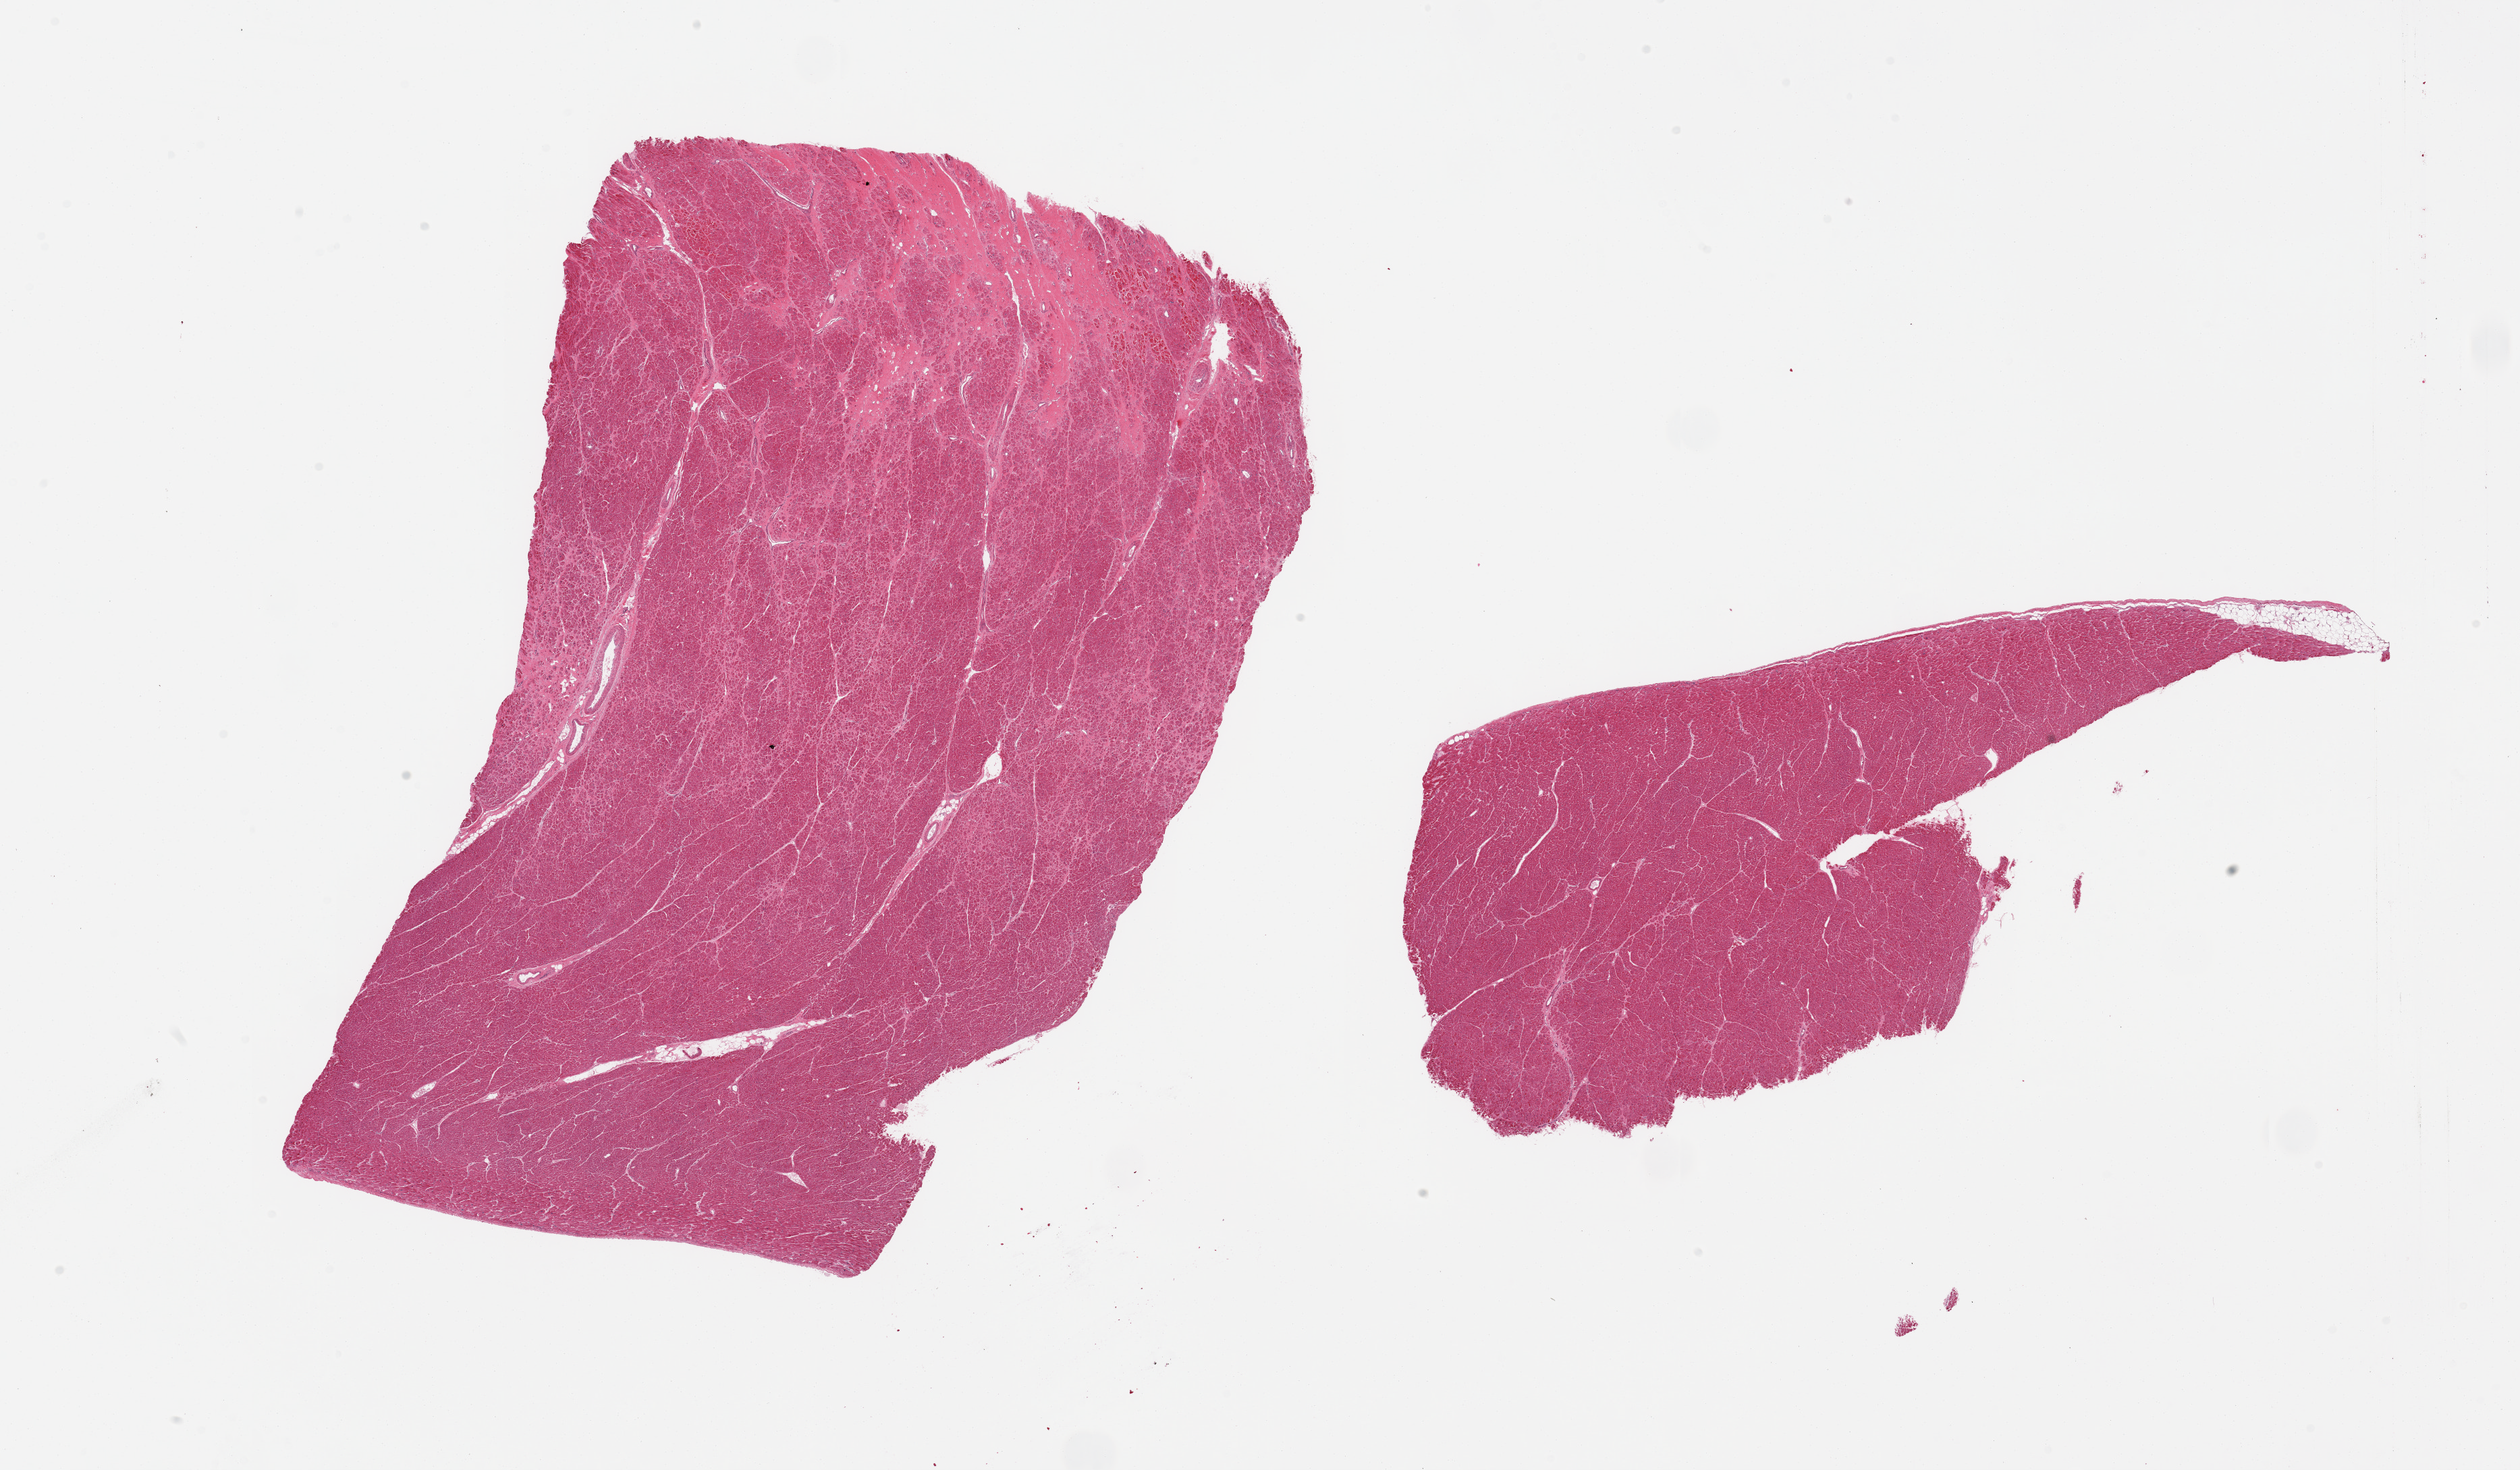
H&E whole-slide image, a low-resolution overview of the entire scanned area, about 29.5 x 17.2 mm, PAXgene-fixed paraffin-embedded (PFPE) section, section of heart (target tissue), tissue donor sample. Donor: male.
Reviewer comment on this tissue sample: 2 pieces; interstitial fibrosis and scar.